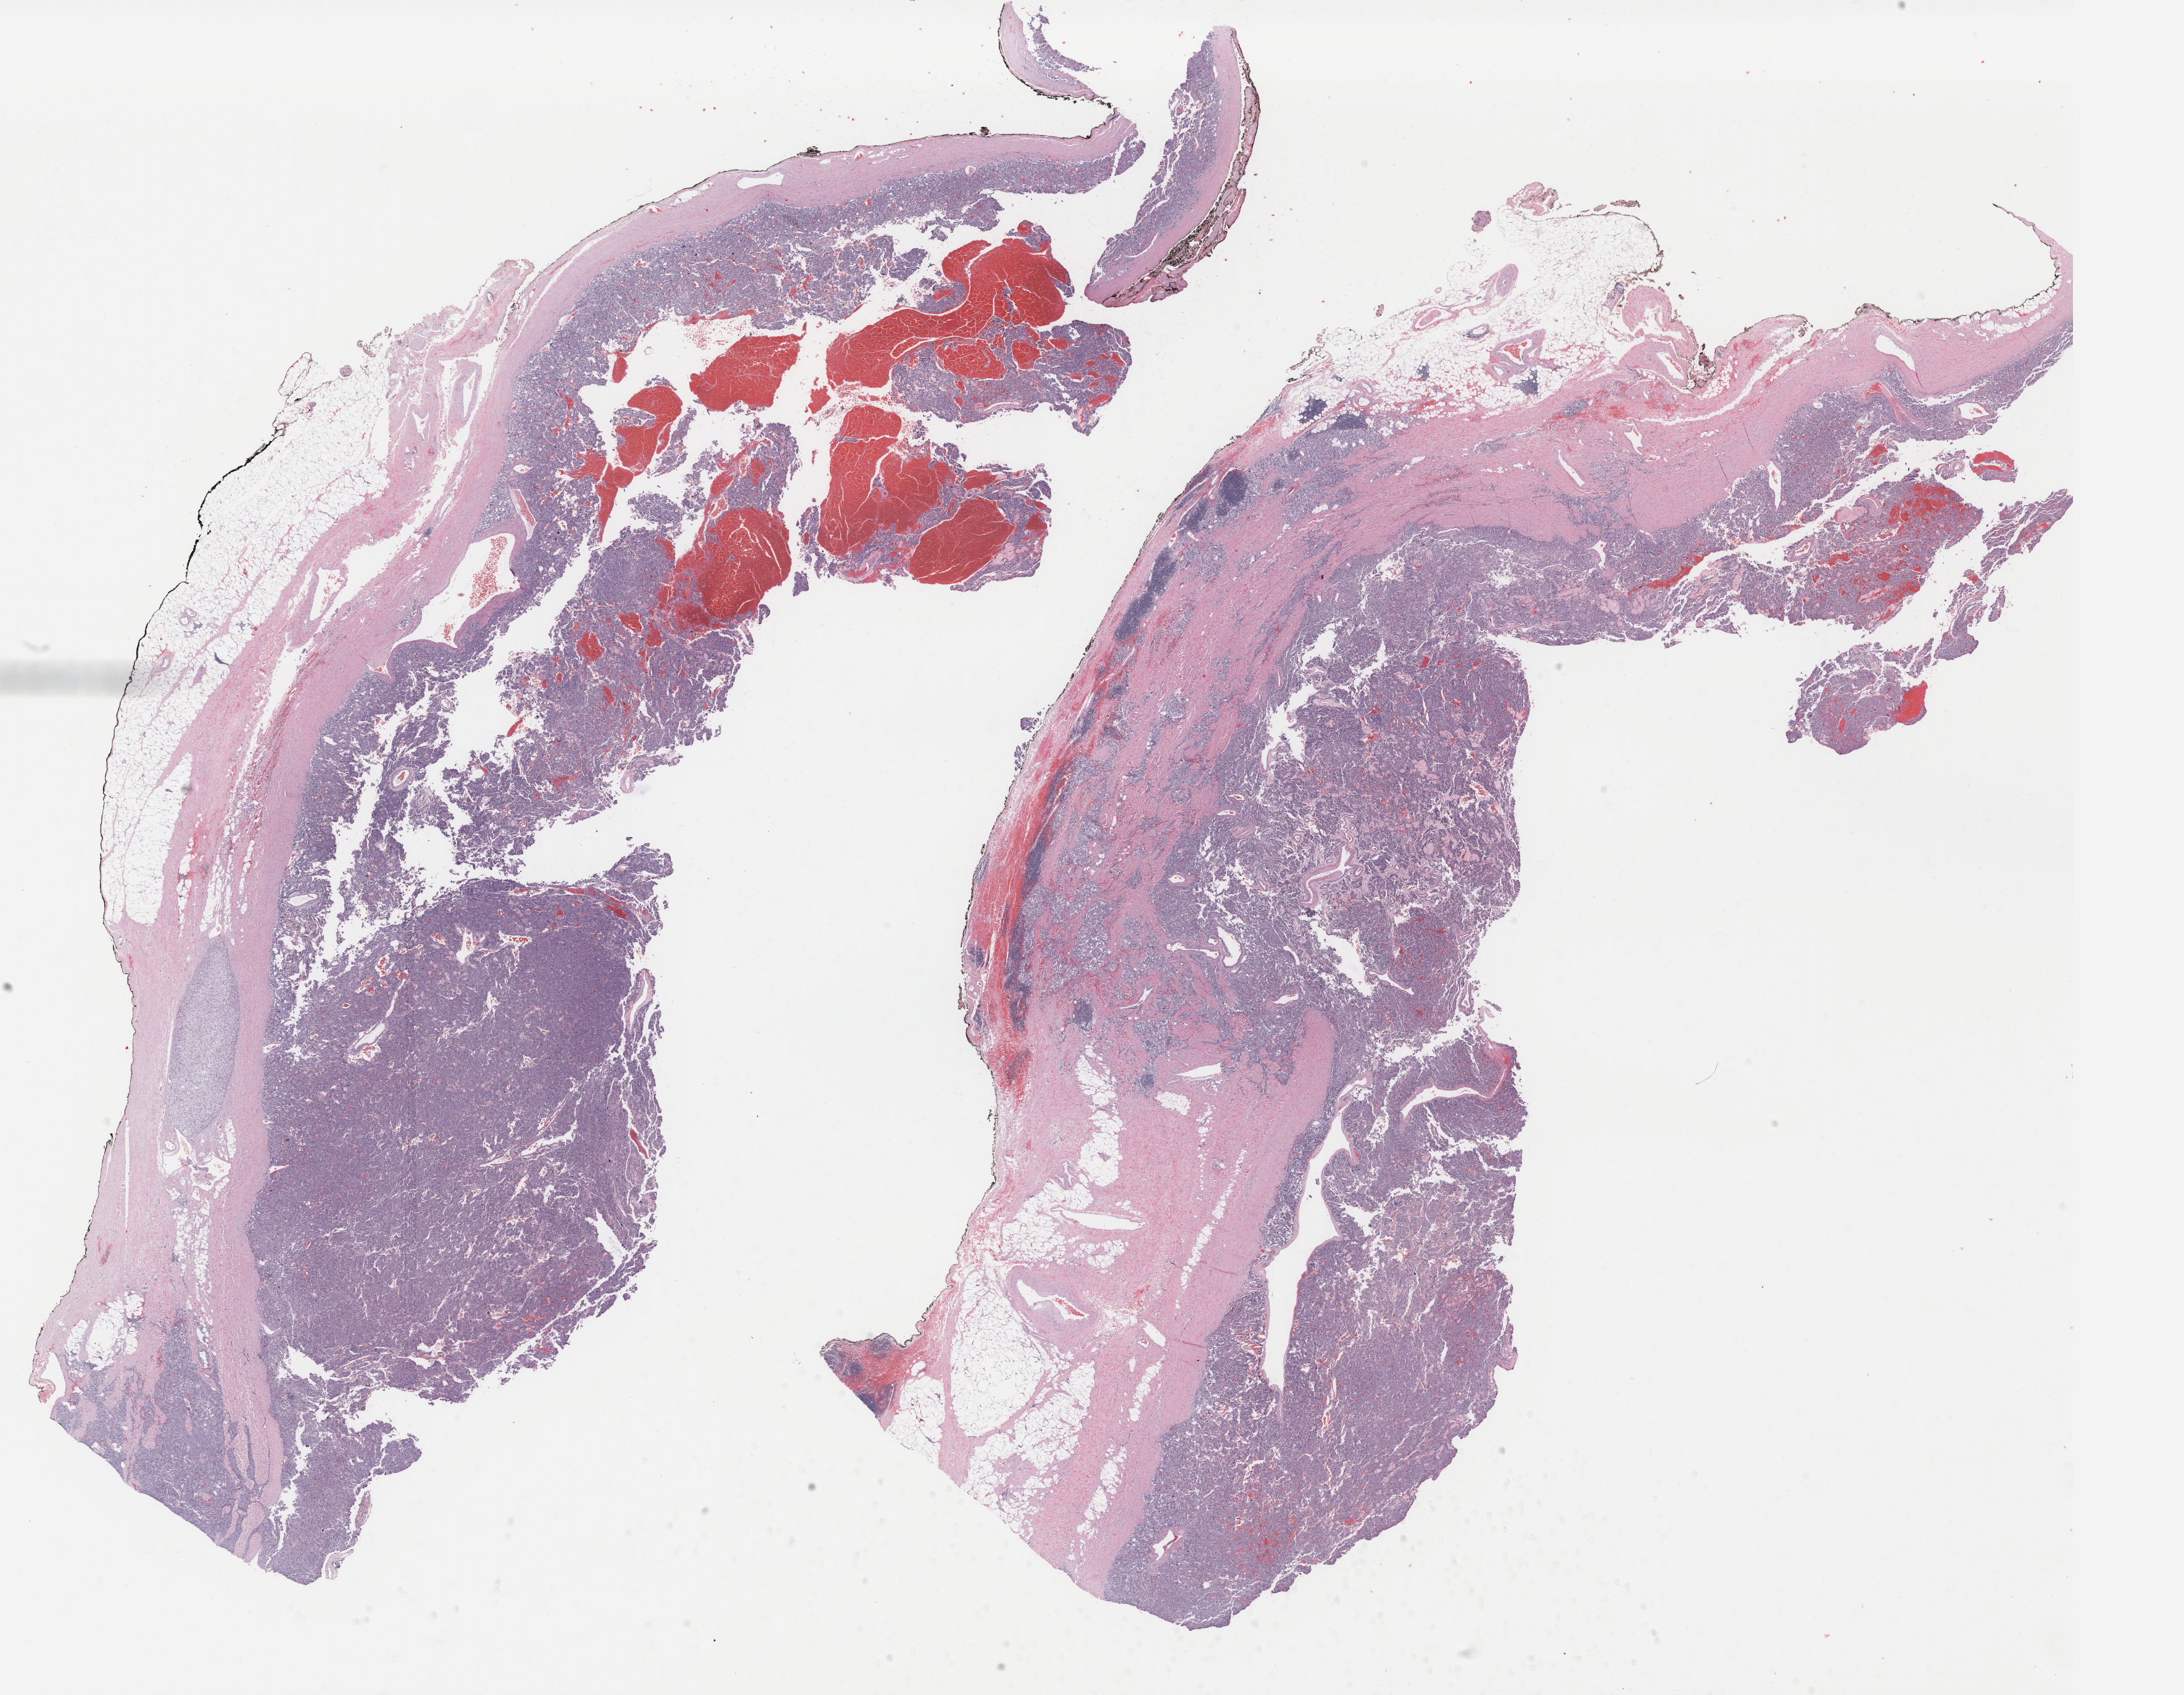
Whole-slide histology image, H&E, a low-resolution overview of the entire scanned area, about 28.1 x 21.8 mm (slide scanned at 40x), FFPE section, primary tumour sample from the adrenal gland. Female, age 62 years at initial diagnosis.
* diagnosis: Pheochromocytoma, malignant